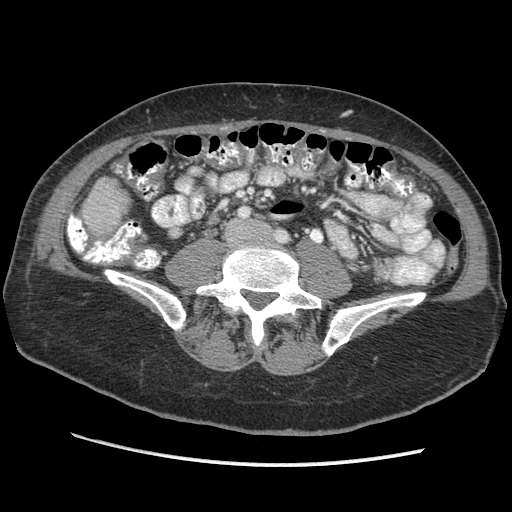
Contrast-enhanced abdominal CT (liver protocol), one axial slice. Slice 79 of 170 in the series (ordered by position). Soft-tissue window (W 400 / L 40 HU). 2.5 mm slice thickness. 512 × 512 image matrix. Case-level facts recorded for this patient, not image findings: diagnosis: hepatocellular carcinoma (patient treated with transarterial chemoembolisation; whether this scan precedes or follows treatment is not stated here); TNM stage (as recorded): Stage-II; Child-Pugh class: A; tumour differentiation: no biopsy; tumour nodularity: multinodular.
Annotated regions visible in this slice (semi-automatically segmented with operator editing):
- liver parenchyma outside the tumour (the mass and vessels are separate outlines, so this box may not span the whole liver): bounding box (x1, y1, x2, y2) in pixels: (82, 178, 128, 236)